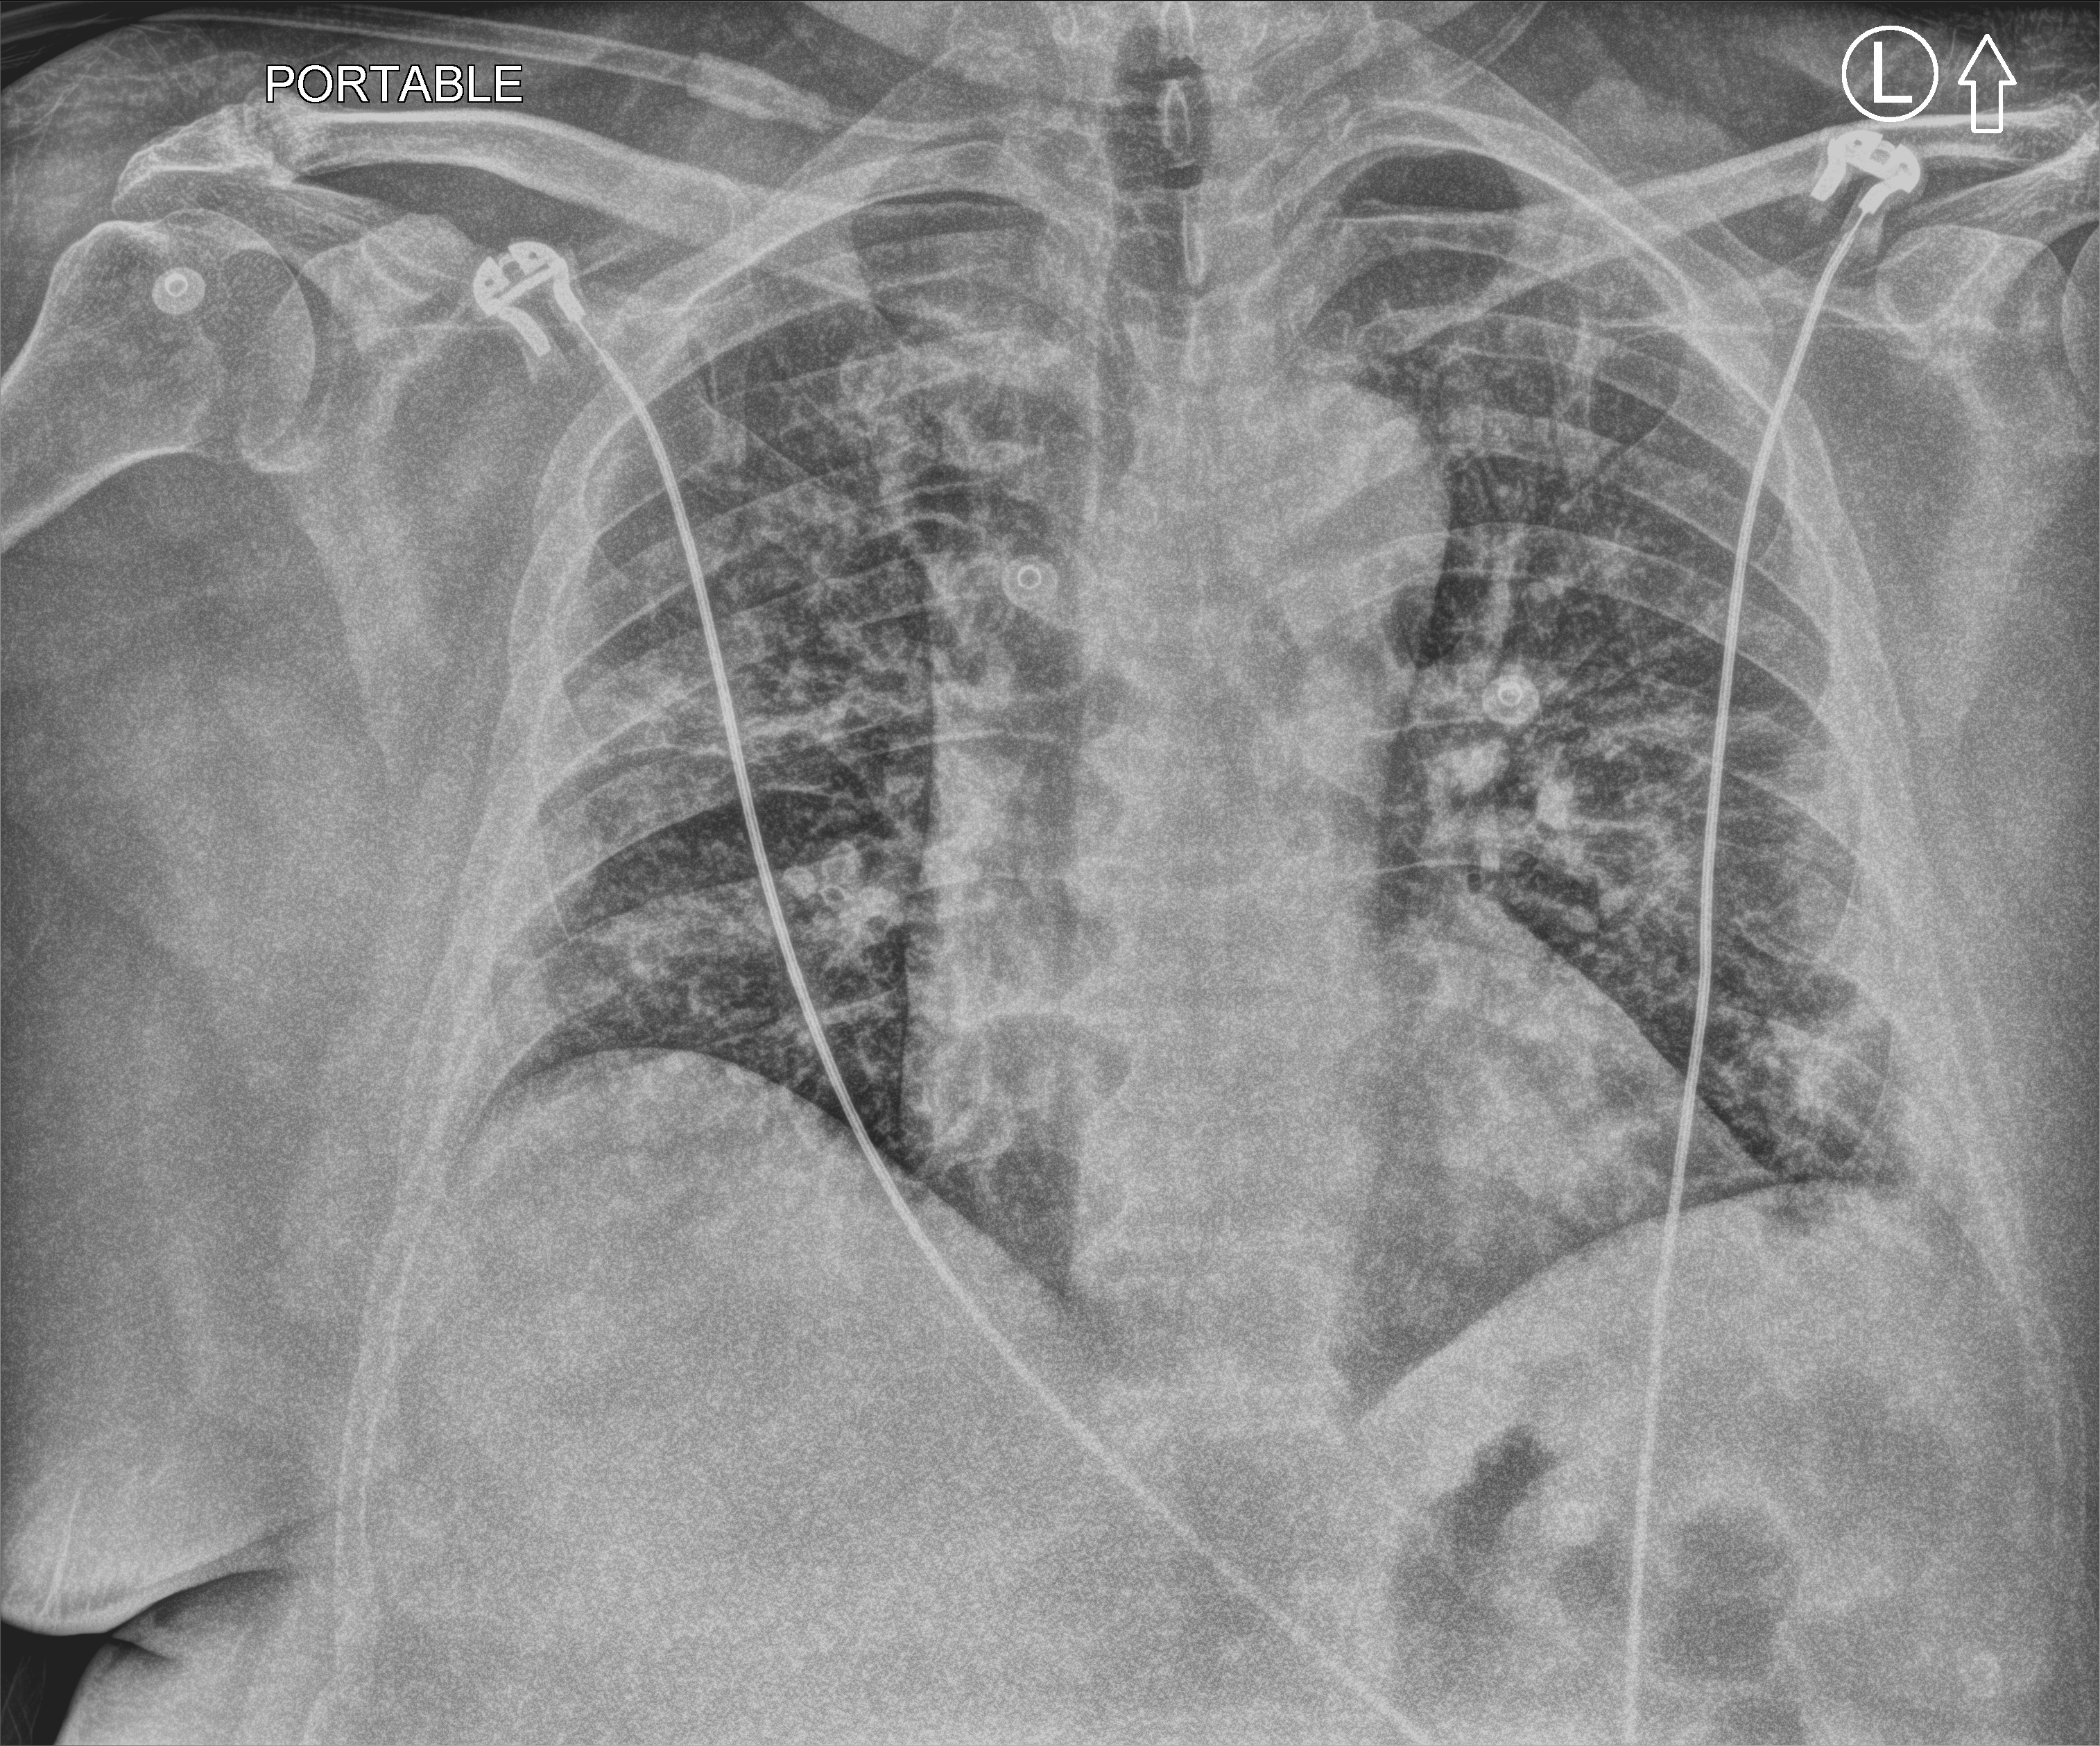
Bedside chest radiograph (computed radiography); anteroposterior (AP) projection. Adult patient hospitalised with COVID-19, age 18–59 years.
Admission-level facts for this patient (not findings on this image; timing relative to this image not recorded): mechanically ventilated during this hospital stay: yes; admitted to intensive care during this hospital stay: yes.